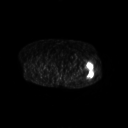
FDG PET of an extremity soft-tissue mass (from a PET/CT study), one axial slice; slice 253 of 267 in the series (ordered by position); 128 × 128 image matrix. Female patient, age 62 years. Case-level facts recorded for this patient, not image findings: histological type: undifferentiated – high grade; grade: high; site of the primary tumour: left thigh.
Structures marked on this image (expert contour drawn on MRI and transferred to this co-registered scan by the dataset authors):
- gross tumour volume including surrounding oedema: bounding box (x1, y1, x2, y2) in pixels: (85, 63, 95, 78)
- gross tumour volume (mass): (86, 63, 94, 78)